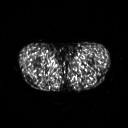
FDG PET of an extremity soft-tissue mass (from a PET/CT study), one axial slice. Position 263 of 311 along the scan axis. 3.27 mm slice thickness. 128 × 128 image matrix, field of view 500 × 500 mm. Patient: male, 29 years. Case-level facts recorded for this patient, not image findings: histological type: mixoid liposarcoma; grade: low; site of the primary tumour: left thigh.
Annotated regions visible in this slice (expert contour drawn on MRI and transferred to this co-registered scan by the dataset authors):
- gross tumour volume (mass): bounding box (x1, y1, x2, y2) in pixels: (76, 59, 81, 63)